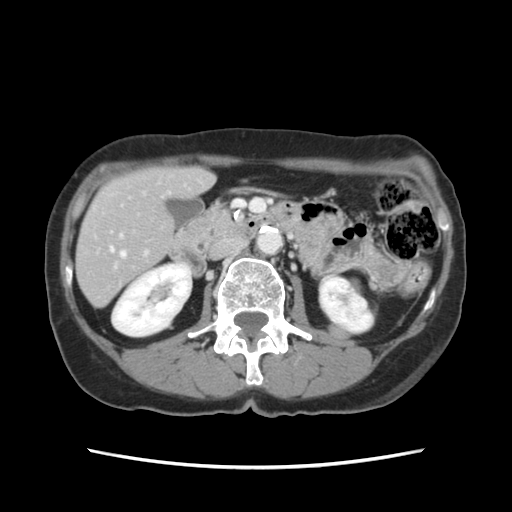
Contrast-enhanced abdominal CT, one axial slice. Intravenous contrast given. Soft-tissue window (W 400 / L 40 HU). 2.5 mm slice thickness. 512 × 512 image matrix, field of view 330 × 330 mm. Female patient, age 70 years. Case-level facts recorded for this patient, not image findings: diagnosis: colorectal cancer liver metastases, imaged before liver resection; multiple liver metastases: no; largest metastasis: 2.5 cm; disease in both lobes: no.
Annotated regions visible in this slice (expert manual segmentation):
- hepatic veins: bounding box (x1, y1, x2, y2) in pixels: (110, 248, 126, 257)
- liver: (77, 168, 213, 305)
- planned liver remnant (the part of the liver to remain after resection): (77, 168, 213, 306)
- portal vein (with intrahepatic branches): (120, 234, 147, 255)